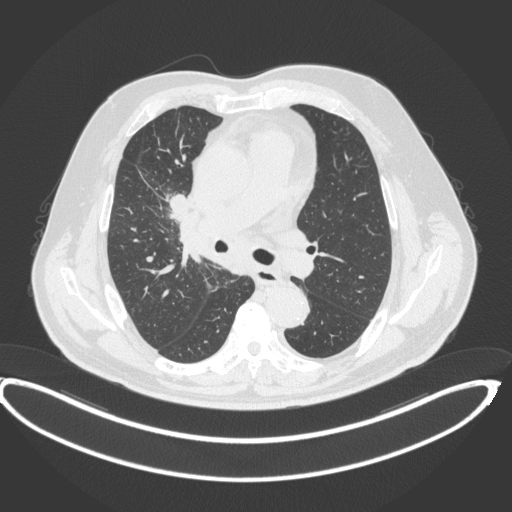
Chest CT, one axial slice. Slice 247 of 395 in the series (ordered by position). Reconstruction kernel B31f. 120 kVp. Lung window (W 1500 / L -600 HU). 512 × 512 image matrix, field of view 448 × 448 mm. Male patient, age 62 years. Case-level facts recorded for this patient, not image findings: clinical TNM (as recorded): T1c N3 M1c.
Annotated regions visible in this slice (rectangle marked by the reading radiologist):
- lung tumour (recorded histology: adenocarcinoma): bounding box <164,188,189,221> (left, top, right, bottom; pixels)